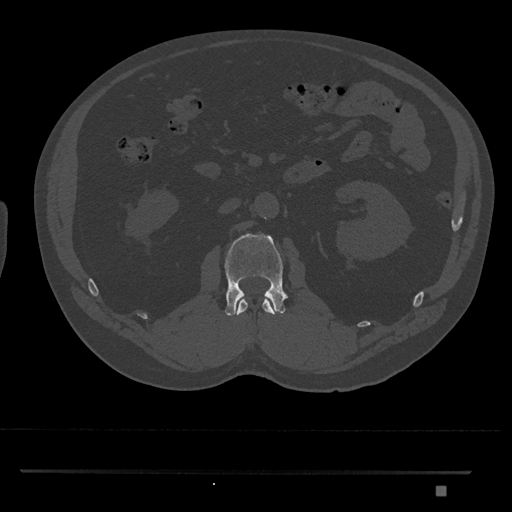
CT including the spine, one axial slice; position 773 of 1134 along the scan axis; reconstruction kernel Br40s/3; 120 kVp; bone window (W 1800 / L 400 HU); 512 × 512 image matrix, field of view 429 × 429 mm. Patient: male, 65 years. From the clinical record (not read from this slice): primary cancer: prostate.
Structures marked on this image (semi-automatically segmented with operator editing):
- L1 vertebra: bounding box (x1, y1, x2, y2) in pixels: (237, 299, 275, 316)
- L2 vertebra: (224, 233, 288, 316)